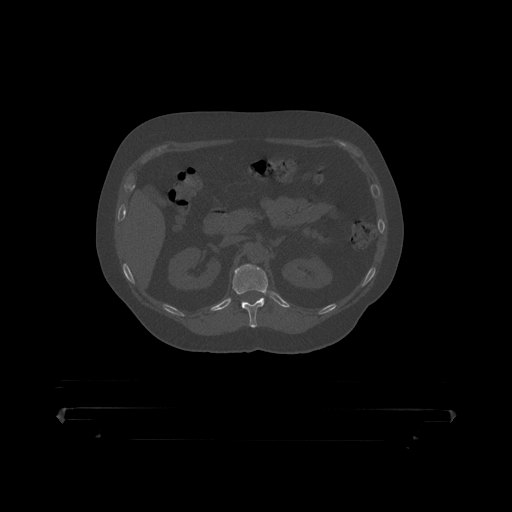
CT including the spine, one axial slice. Position 166 of 390 along the scan axis. Bone window (W 1800 / L 400 HU). 1.25 mm slice thickness. 512 × 512 image matrix, field of view 650 × 650 mm. Male patient, age 60 years. Case-level facts recorded for this patient, not image findings: primary cancer: prostate.
Outlined on this slice (semi-automatically segmented with operator editing):
- T12 vertebra: box from (x=233, y=265) to (x=268, y=319) px